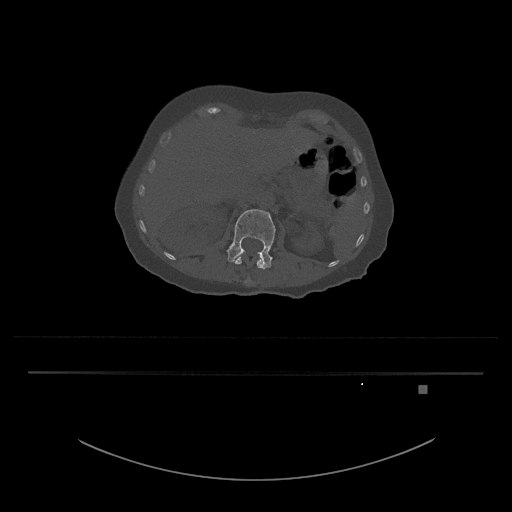
CT including the spine, one axial slice. Position 511 of 797 along the scan axis. Reconstruction kernel Br40s/3. 120 kVp. Bone window (W 1800 / L 400 HU). 0.5 mm slice thickness. 512 × 512 image matrix, field of view 500 × 500 mm. Female patient, age 57 years. Case-level facts recorded for this patient, not image findings: primary cancer: cervical.
Outlined on this slice (semi-automatic segmentation, software-assisted and operator-edited):
- L1 vertebra: bounding box <235,254,264,282> (left, top, right, bottom; pixels)